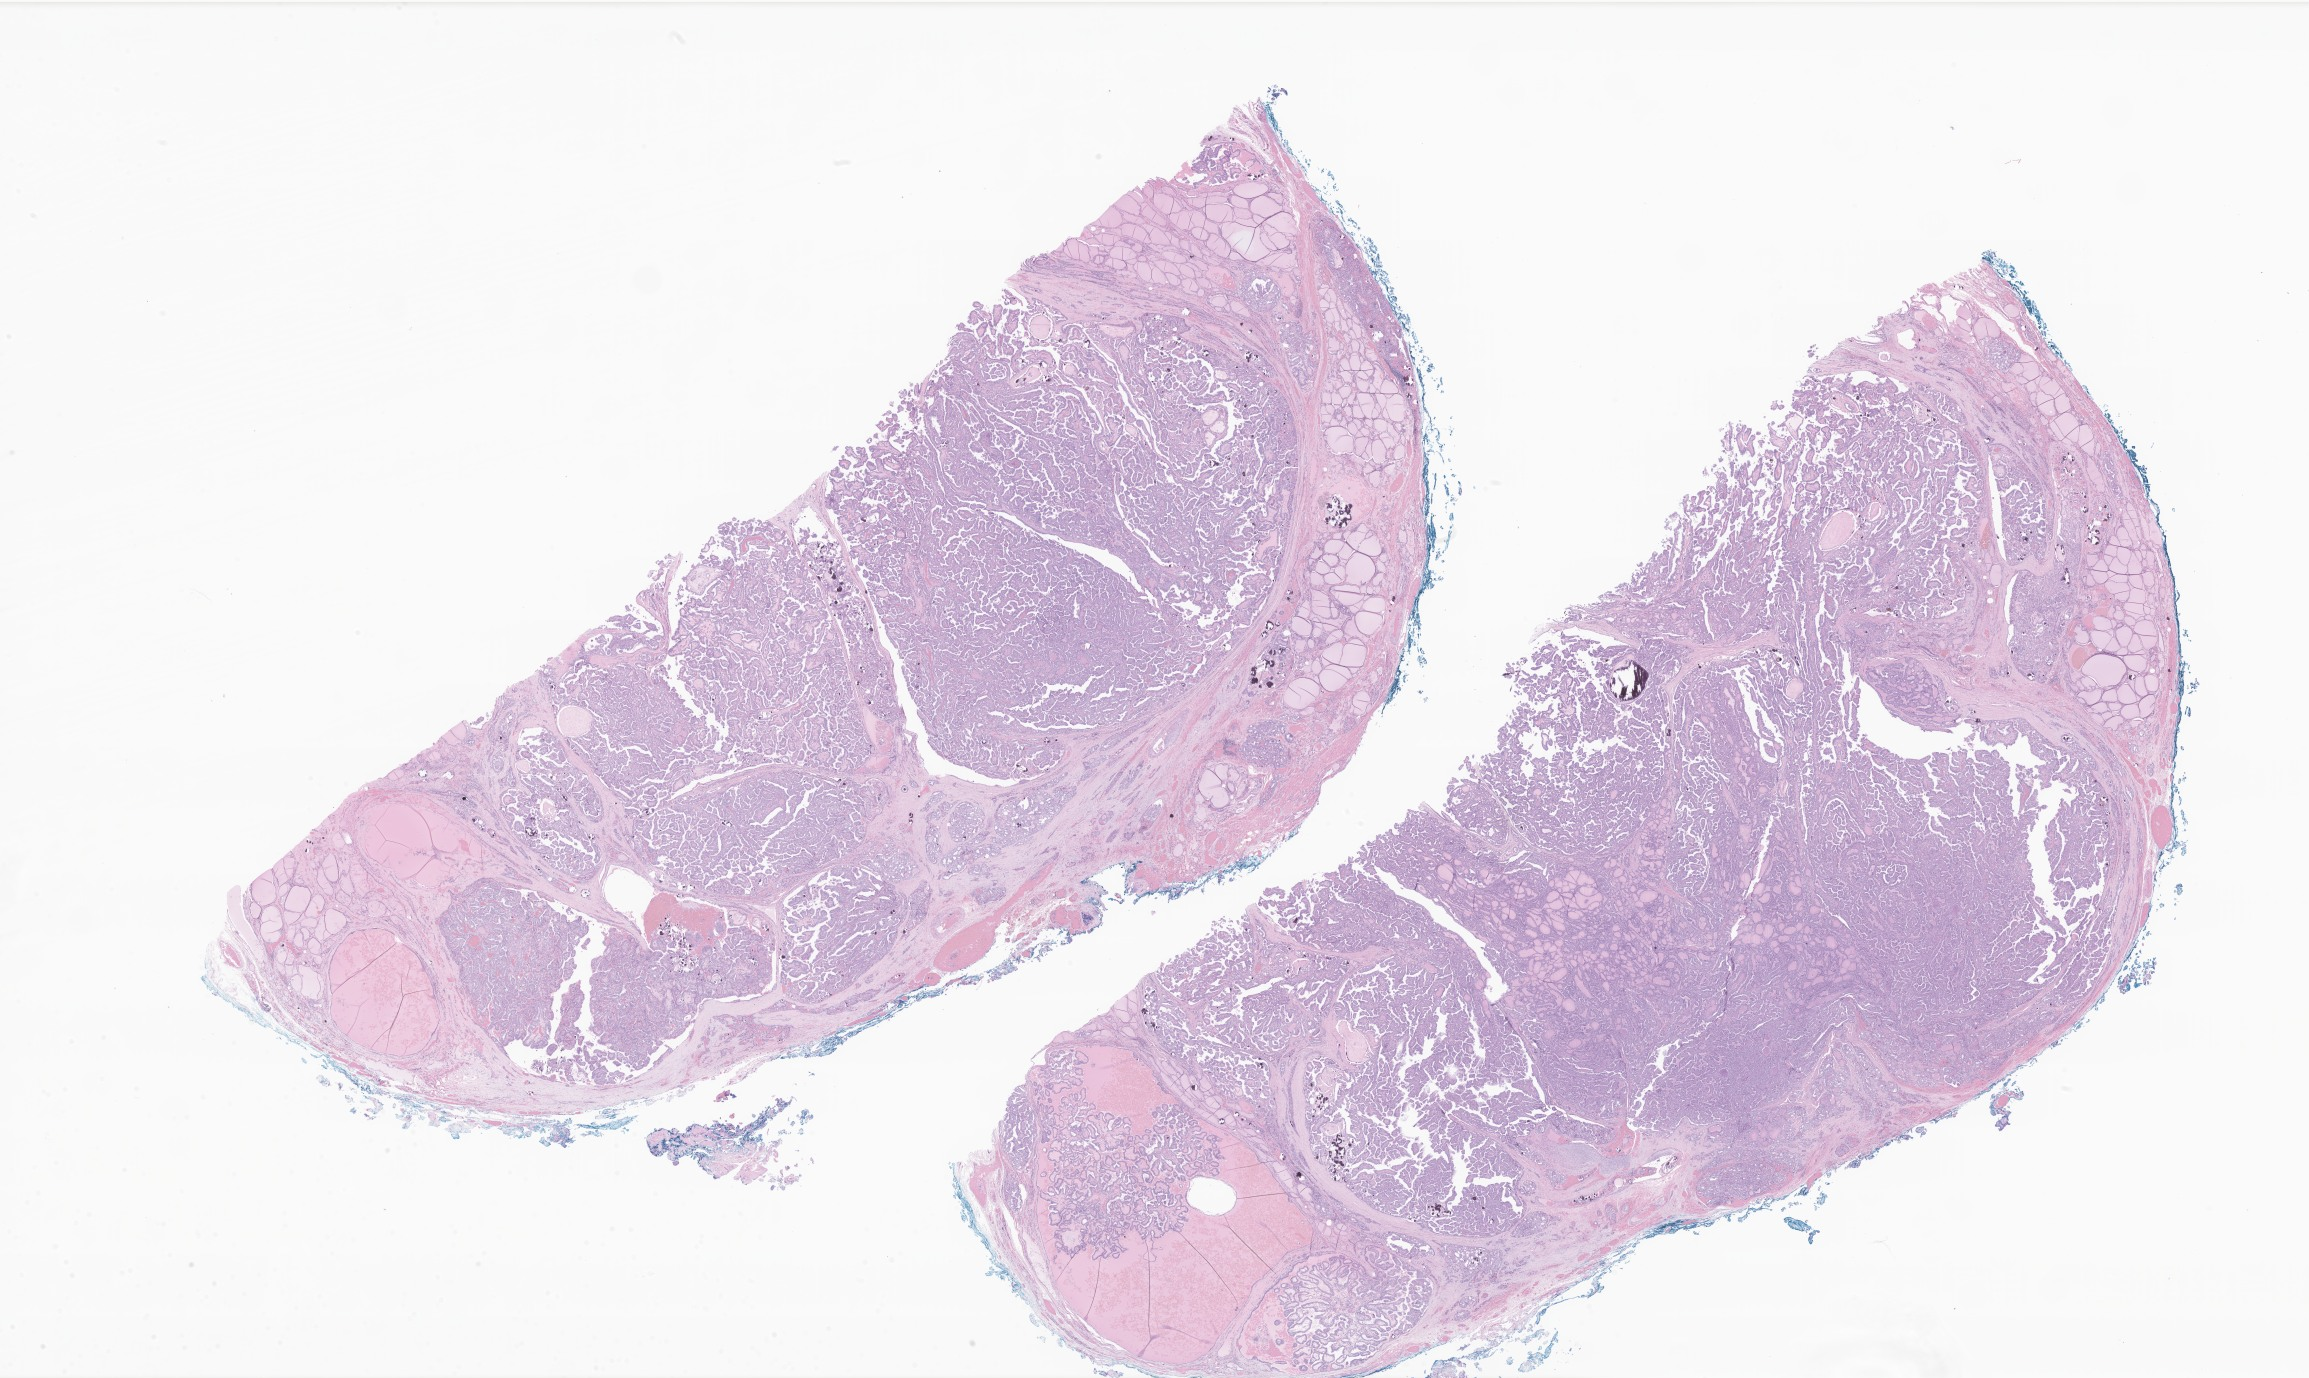
Hematoxylin and eosin (H&E) whole-slide image of tumor tissue from the thyroid — a low-resolution overview of the entire scanned area, about 38.9 x 23.2 mm. FFPE section. Female patient, age 202 months.
Recorded diagnosis: Papillary adenocarcinoma, NOS.